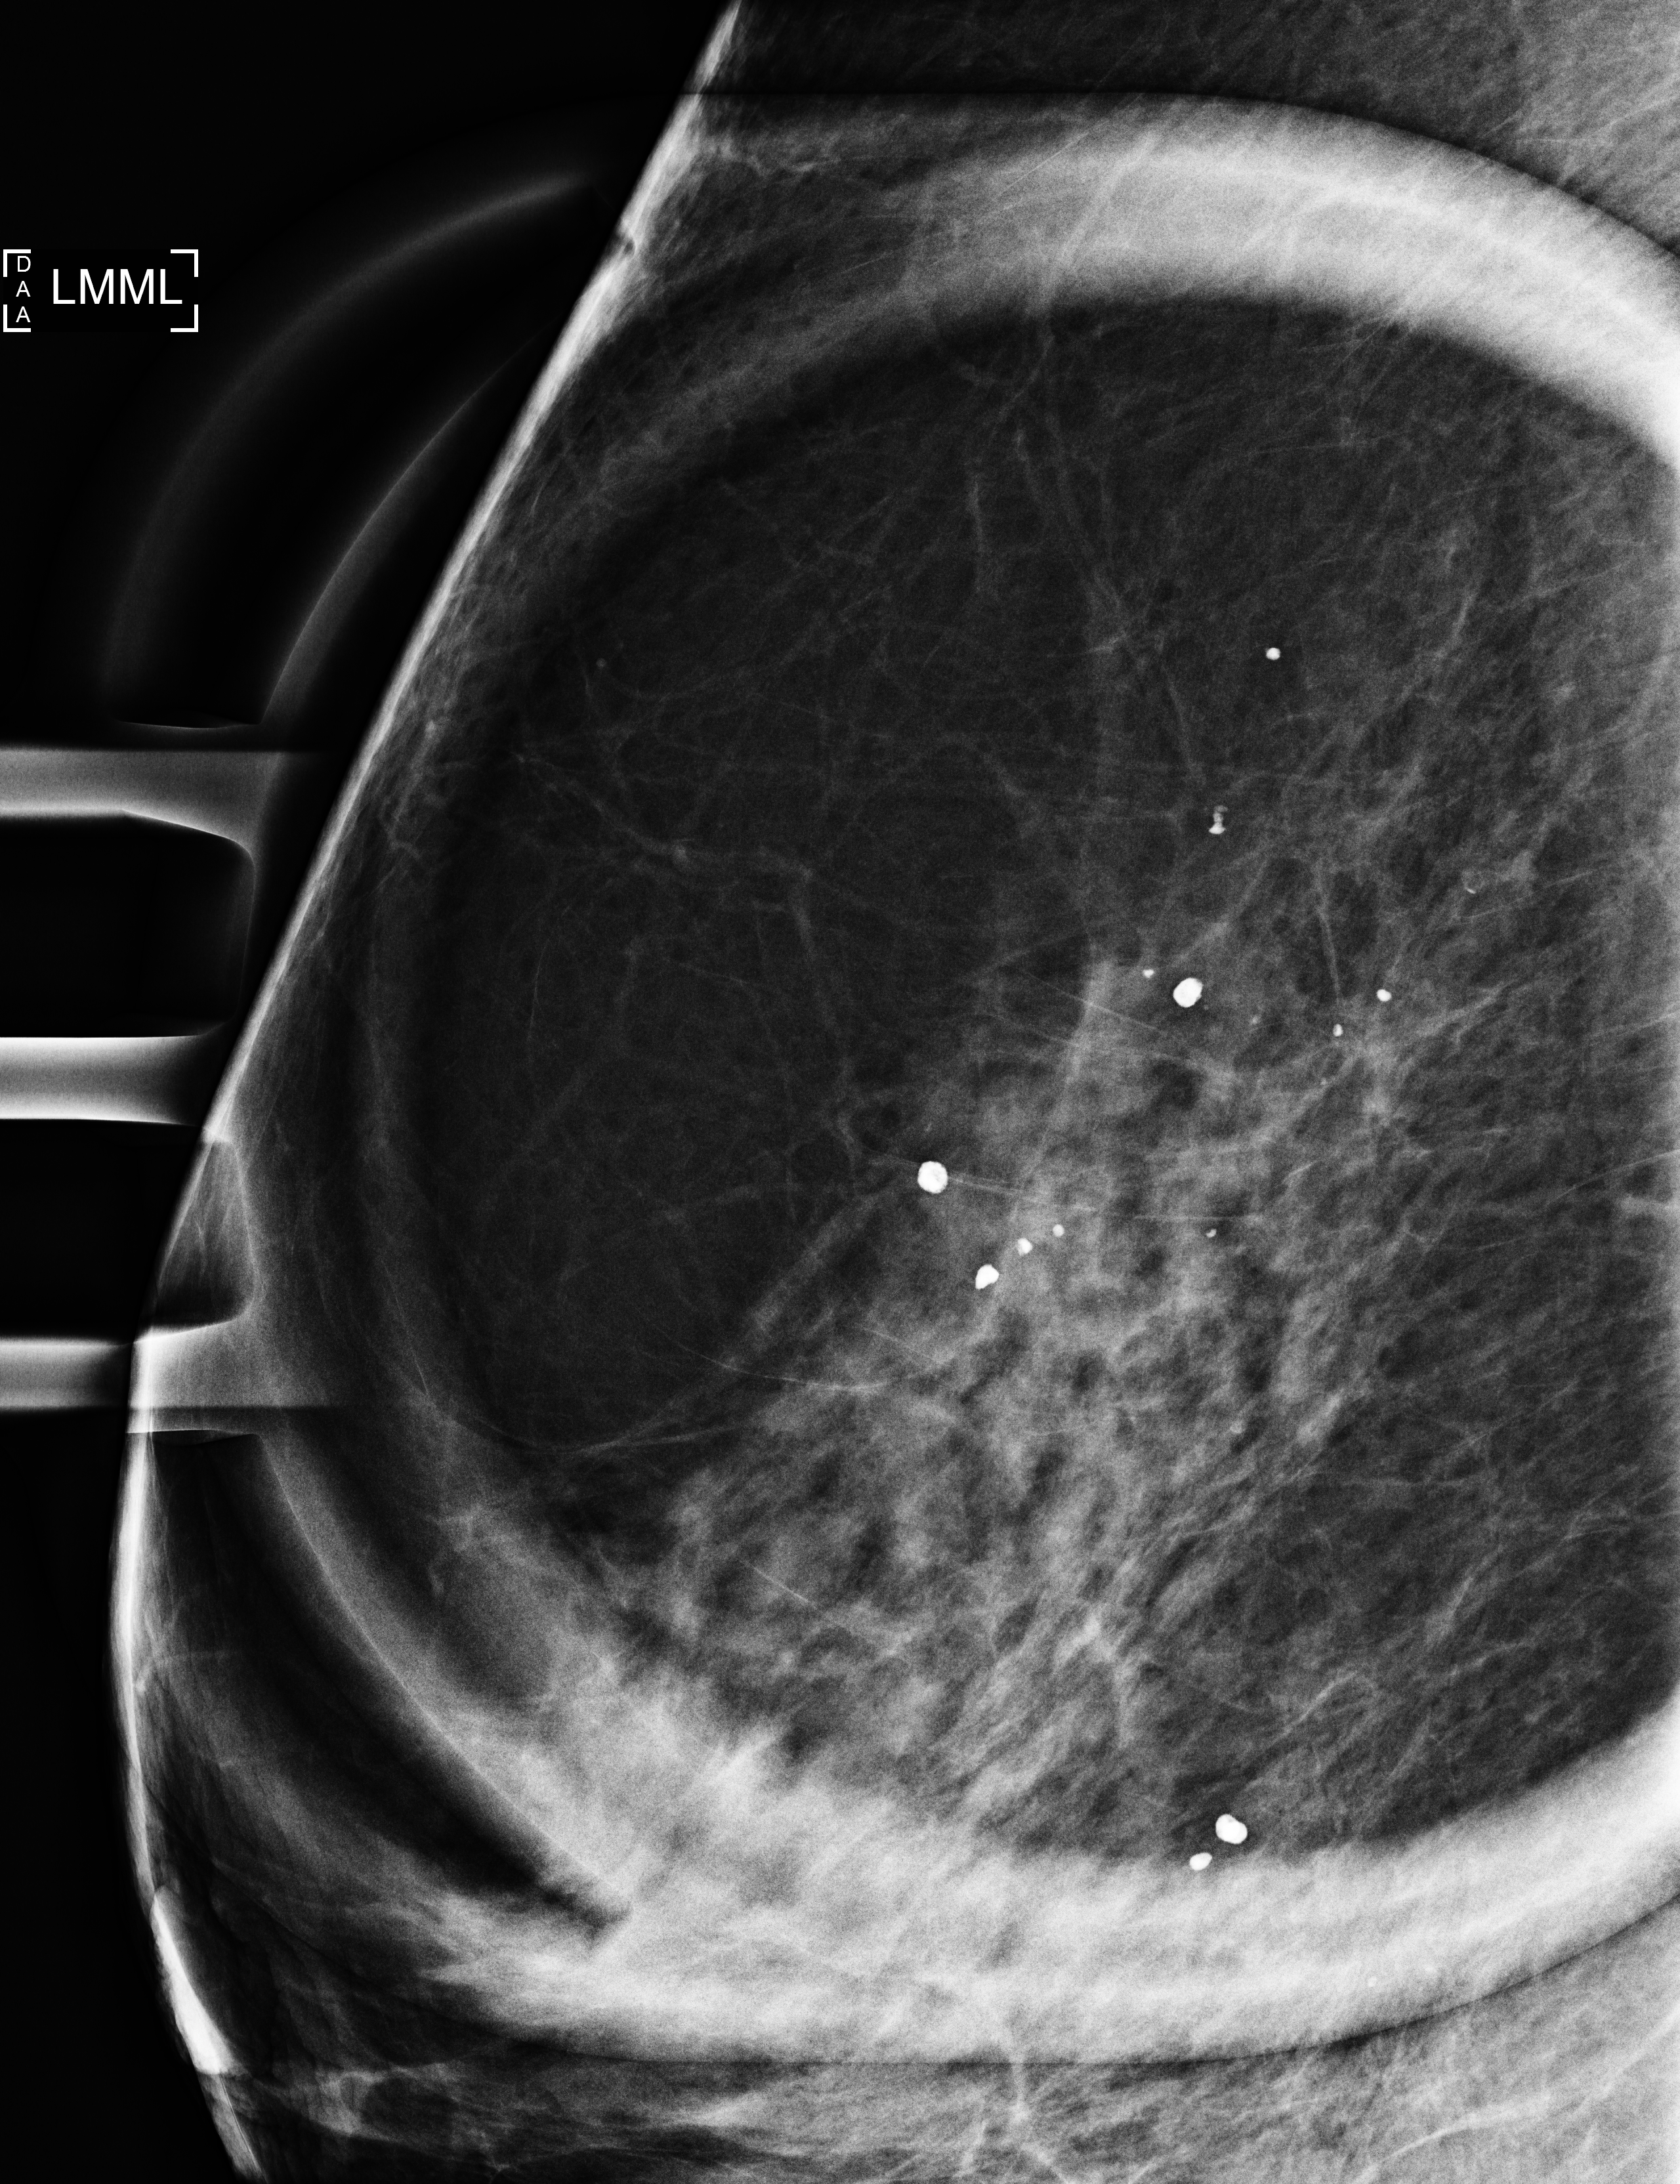
Additional work-up view, compressed breast thickness 66 mm. Female patient, age 49 years.
Image type: full-field digital mammogram. Breast: left. Projection: ML view, magnification. BI-RADS breast density category at the screening exam (both breasts, scale 1–4): 3. Final BI-RADS assessment for this screening round (tomosynthesis exam, both breasts): category 2. Recall: recalled for additional imaging after this screen.